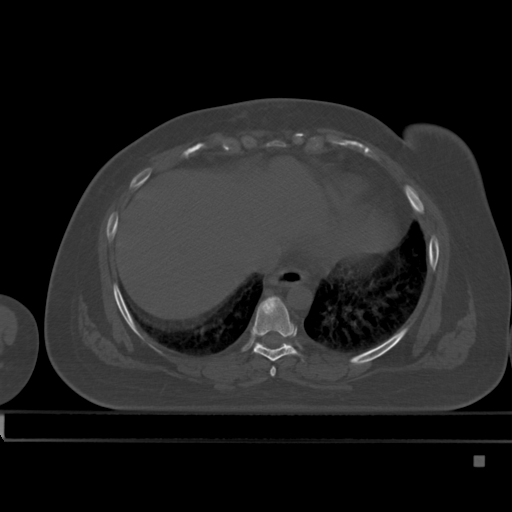
CT including the spine, one axial slice; slice 275 of 495 in the series (ordered by position); bone window (W 1800 / L 400 HU); 1.5 mm slice thickness; 512 × 512 image matrix. Patient: female, 33 years. Case-level facts recorded for this patient, not image findings: primary cancer: breast.
Outlined on this slice (semi-automatically segmented with operator editing):
- T7 vertebra: box from (x=270, y=367) to (x=276, y=377) px
- T8 vertebra: (x=244, y=295)–(x=297, y=362)
- T9 vertebra: (x=254, y=342)–(x=256, y=345)